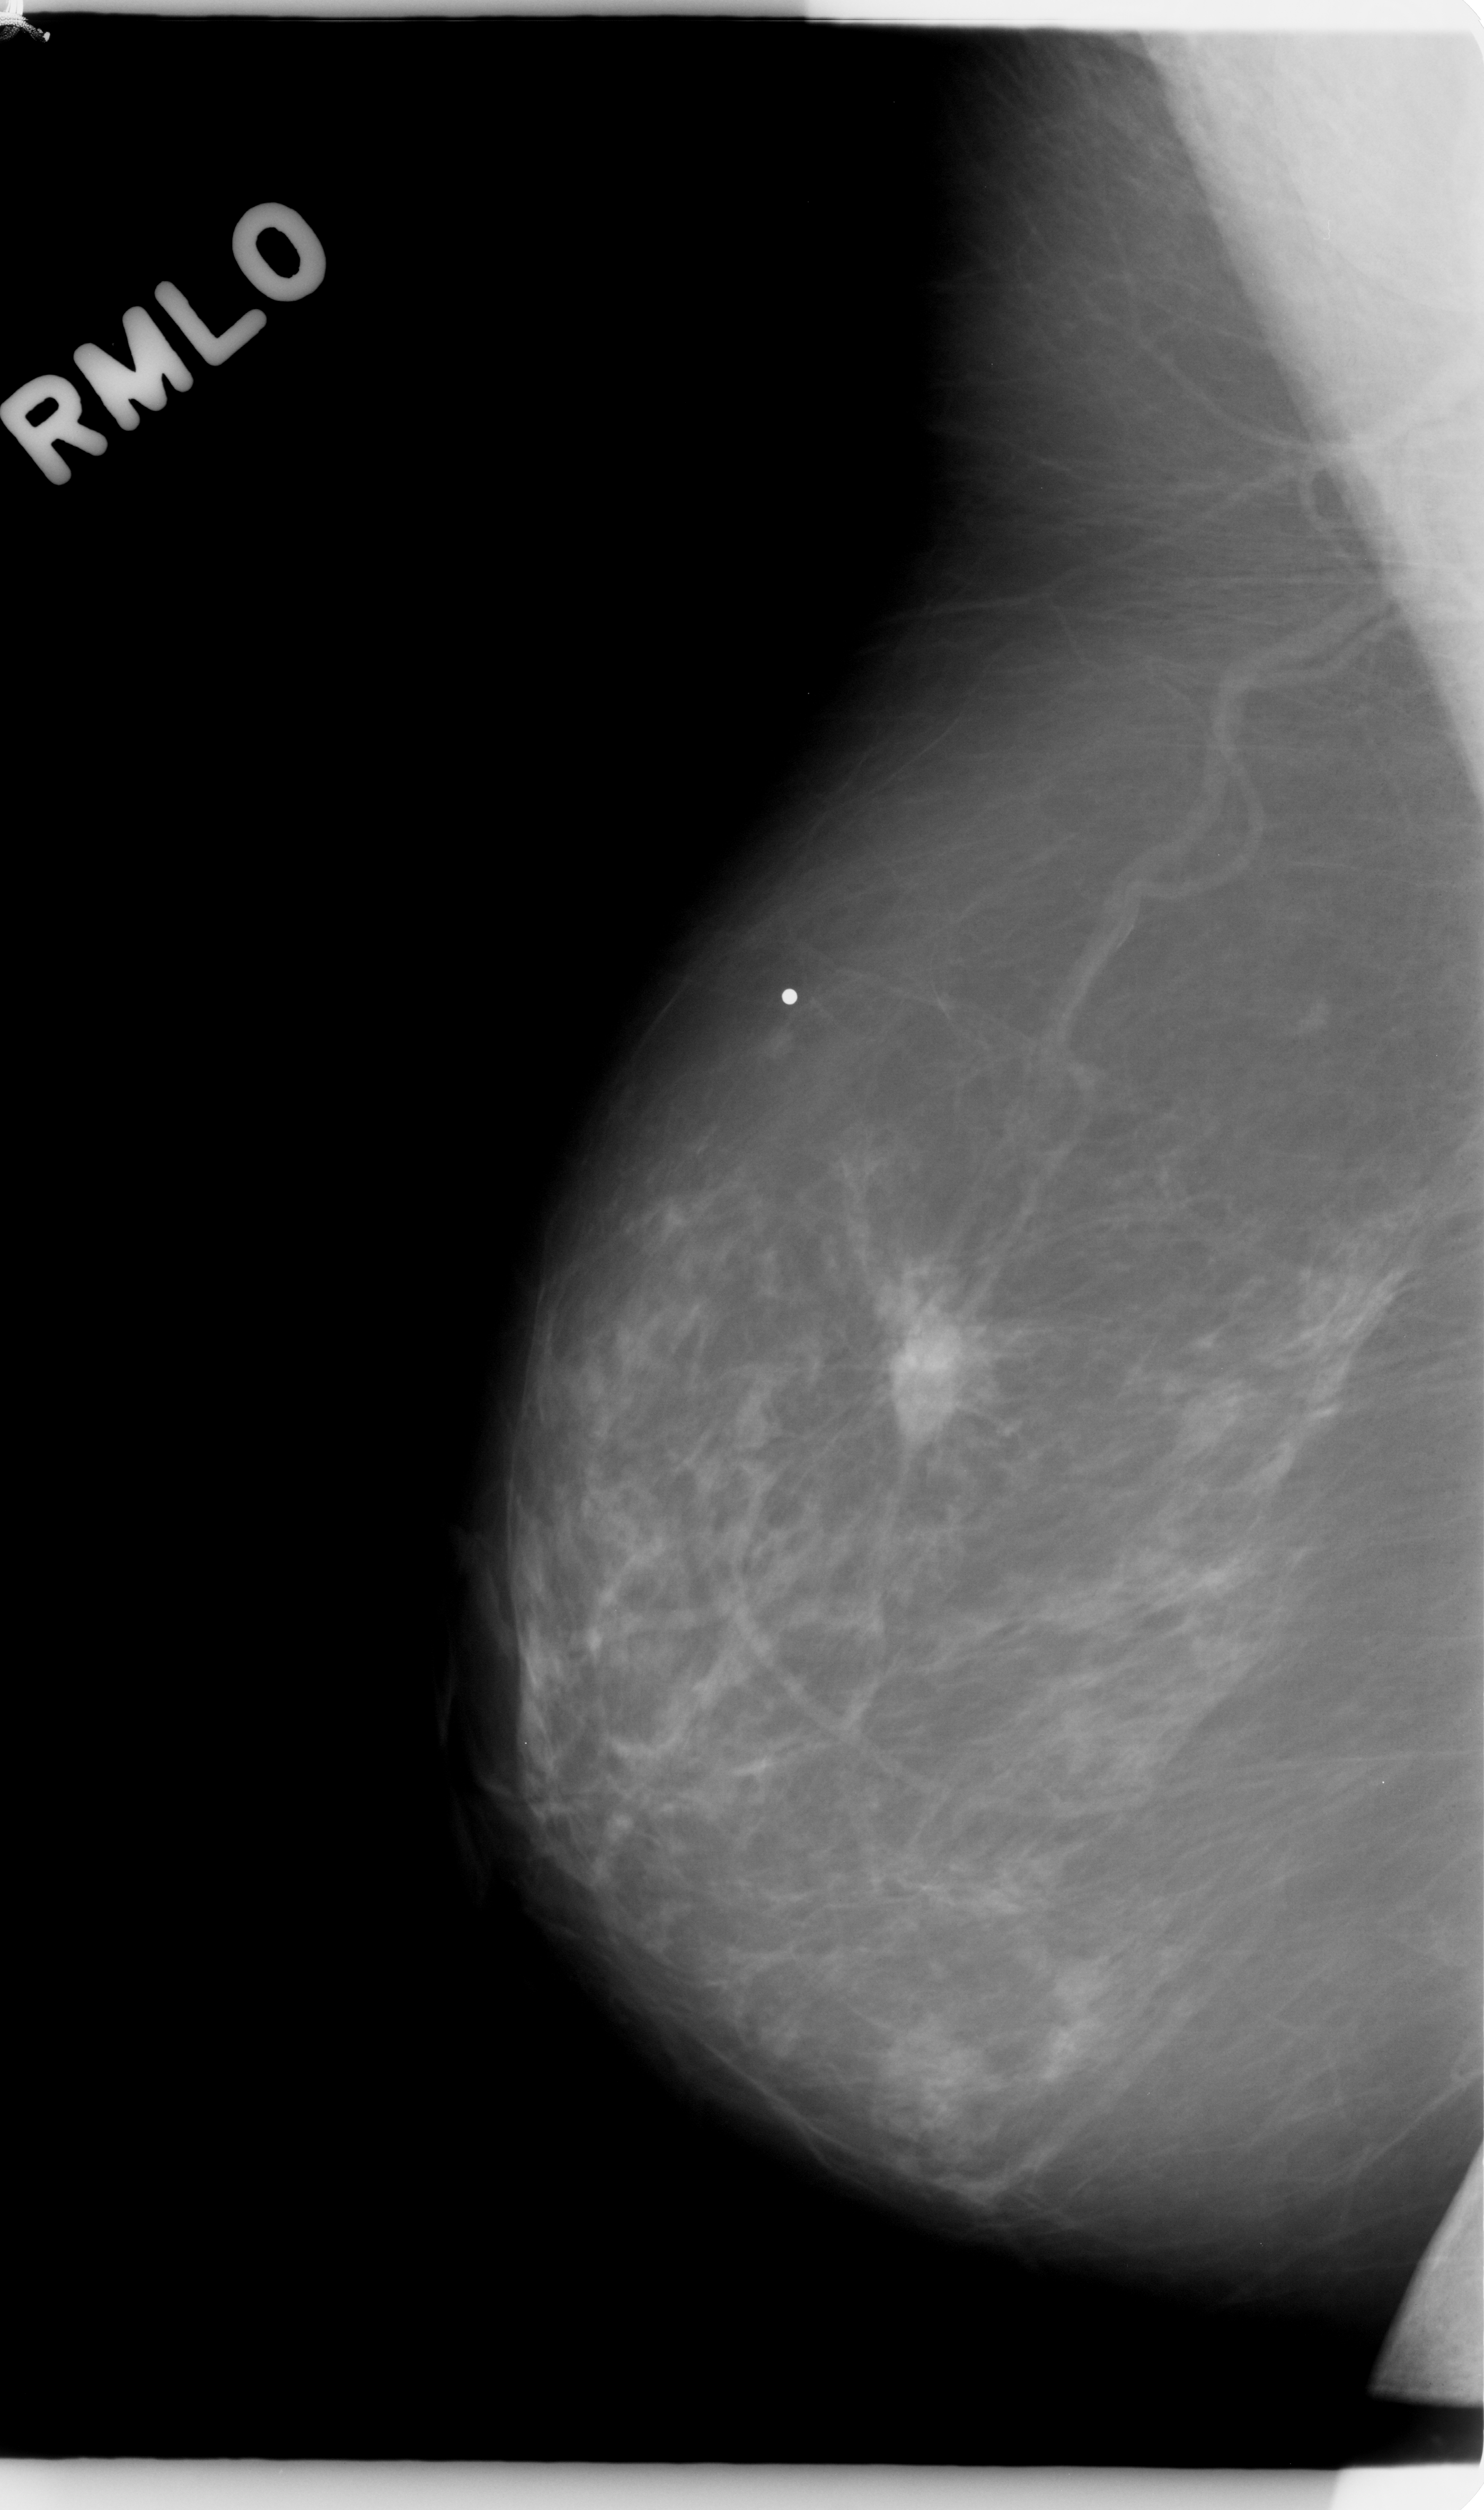
Scanned film-screen mammogram. Right breast. Mediolateral oblique (MLO) view. Breast composition: almost entirely fatty (BI-RADS density category 1 of 4). 1484 × 2510 image matrix.
Expert-marked regions of interest on this film, with their recorded descriptors:
- mass, shape irregular, margins spiculated; BI-RADS assessment category 5; pathology (as recorded): malignant: bounding box <870,1278,1010,1449> (left, top, right, bottom; pixels)